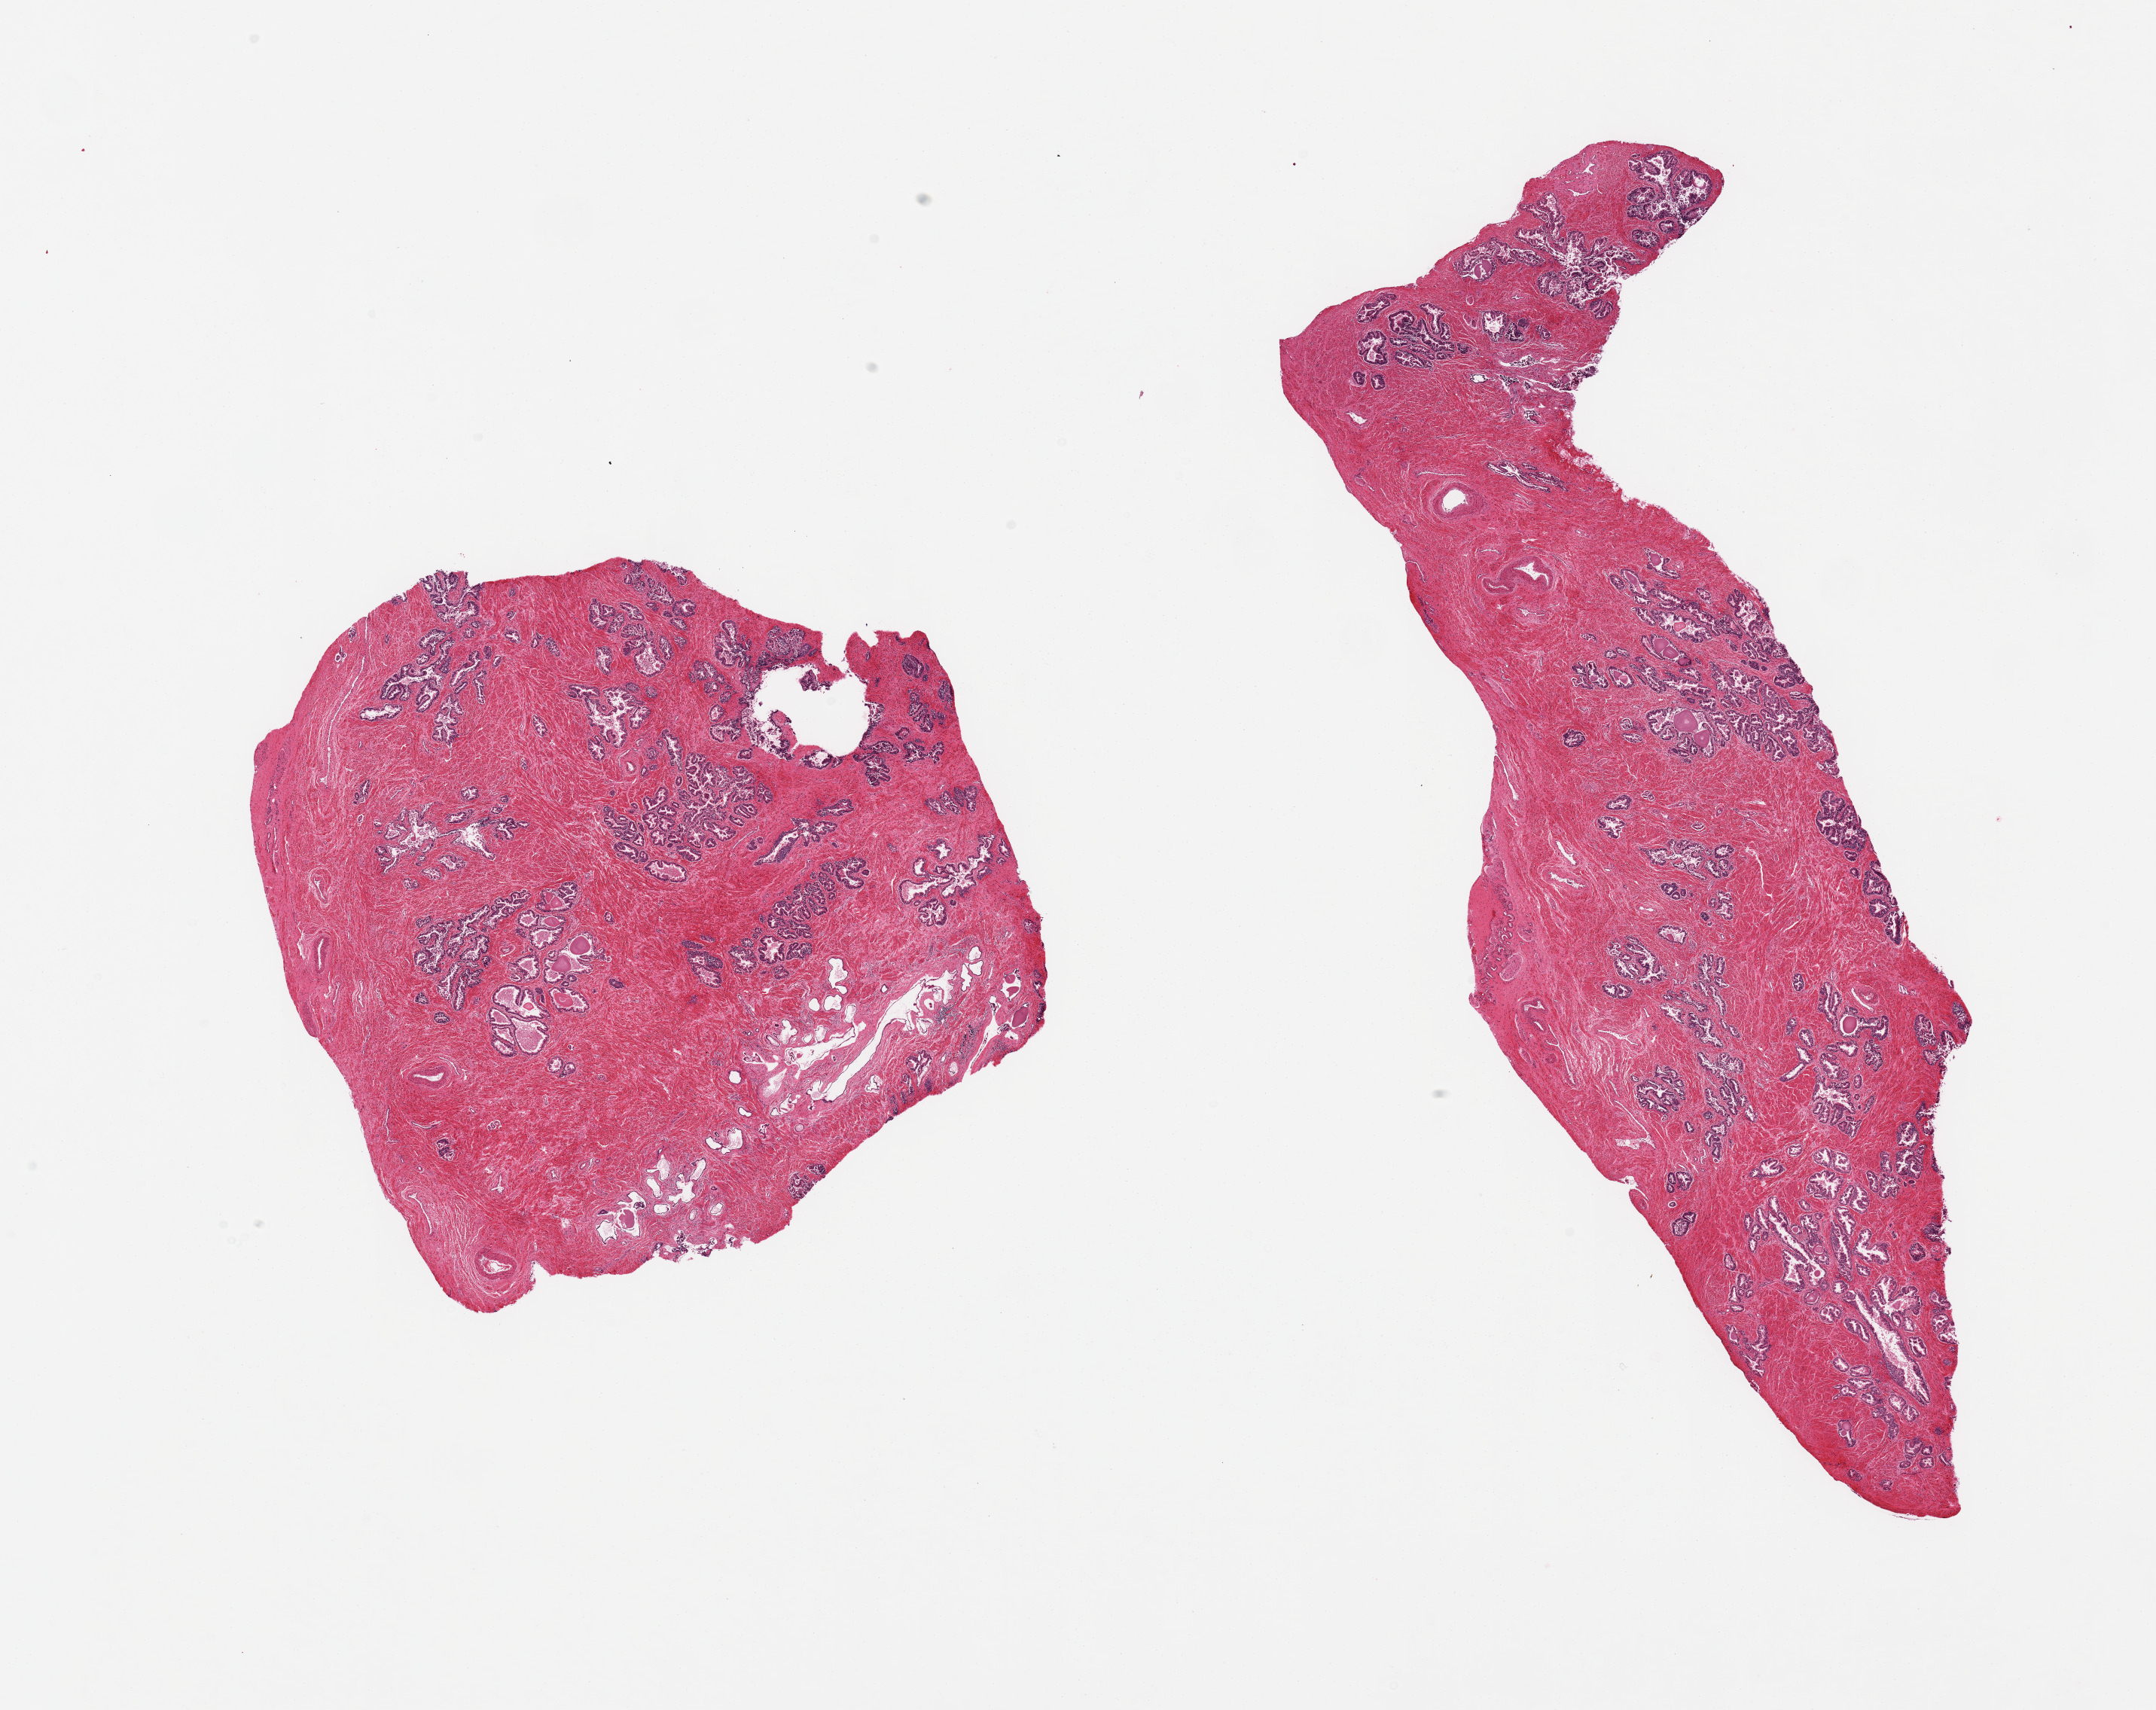
Whole-slide image, haematoxylin and eosin stain, whole scanned area (about 22.6 x 18.0 mm) shown as a low-resolution overview; PAXgene-fixed paraffin-embedded (PFPE) section; section of prostate (target tissue); tissue donor sample. Male donor.
Review note (as recorded): 2 pieces, mild glandular hyperplasia.